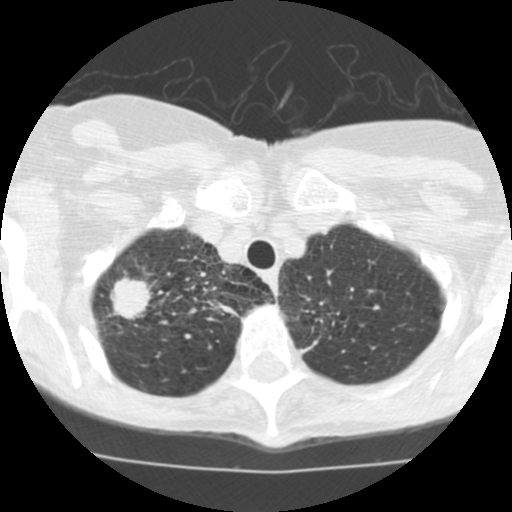
Low-dose screening chest CT, one axial slice. Position 99 of 115 along the scan axis. 120 kVp. Lung window (W 1500 / L -600 HU). 2.5 mm slice thickness. 512 × 512 image matrix.
Annotated regions visible in this slice (manually delineated by an expert):
- lesion 1 (tumor, upper lobe of right lung): bounding box (x1, y1, x2, y2) in pixels: (110, 276, 152, 320)